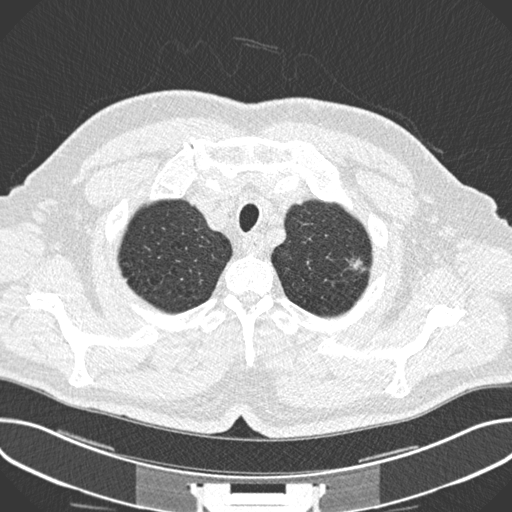
Chest CT (low-dose screening protocol), one axial image; baseline screening round; lung window (W 1500 / L -600 HU); 2 mm slice thickness; standard (soft-tissue) reconstruction kernel (B30f); slice 28 of 245 in the series. Male participant, aged 63 years at enrolment. Current smoker at enrolment.
Expert reader's lesion annotation, bounding box <340,250,377,281> (left, top, right, bottom; pixels). The screening reader recorded 2 non-calcified nodules or masses ≥4 mm on this exam (left upper lobe, left upper lobe); which of them this box marks is not recorded. Later outcome: lung cancer diagnosed 174 days after this screen — adenocarcinoma, NOS, left upper lobe, poorly differentiated (G3), stage IIIA (AJCC 6th edition), 11 mm at pathology.